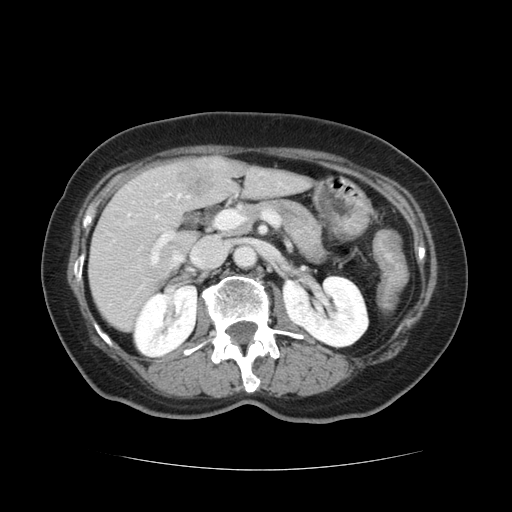
Contrast-enhanced abdominal CT, one axial slice; position 57 of 128 along the scan axis; 120 kVp; soft-tissue window (W 400 / L 40 HU); 2.5 mm slice thickness; 512 × 512 image matrix, field of view 366 × 366 mm. Female patient, age 67 years. Case-level facts recorded for this patient, not image findings: diagnosis: colorectal cancer liver metastases, imaged before liver resection; multiple liver metastases: yes; largest metastasis: 3 cm; disease in both lobes: yes.
Structures marked on this image (expert manual segmentation):
- hepatic veins: bounding box [x1, y1, x2, y2] px = [172, 253, 183, 265]
- liver: [90, 159, 307, 330]
- planned liver remnant (the part of the liver to remain after resection): [90, 167, 307, 330]
- portal vein (with intrahepatic branches): [140, 212, 241, 265]
- liver metastasis: [178, 162, 215, 198]